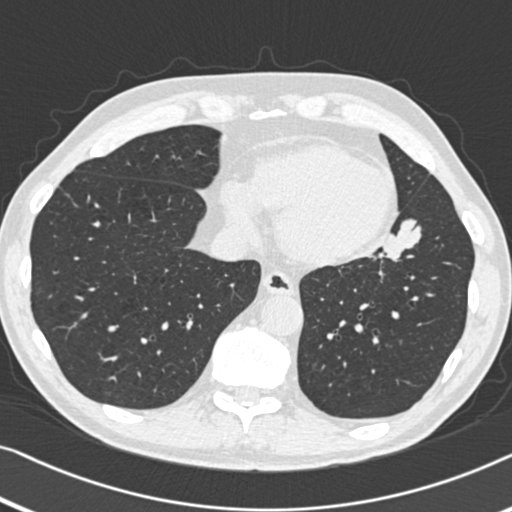
Low-dose screening chest CT, one axial slice; slice 137 of 383 in the series (ordered by position); lung window (W 1500 / L -600 HU); 1 mm slice thickness; 512 × 512 image matrix, field of view 332 × 332 mm.
Annotated regions visible in this slice (outlined manually by an expert reader):
- lesion 1 (tumor, upper lobe of left lung): box from (x=380, y=219) to (x=421, y=261) px